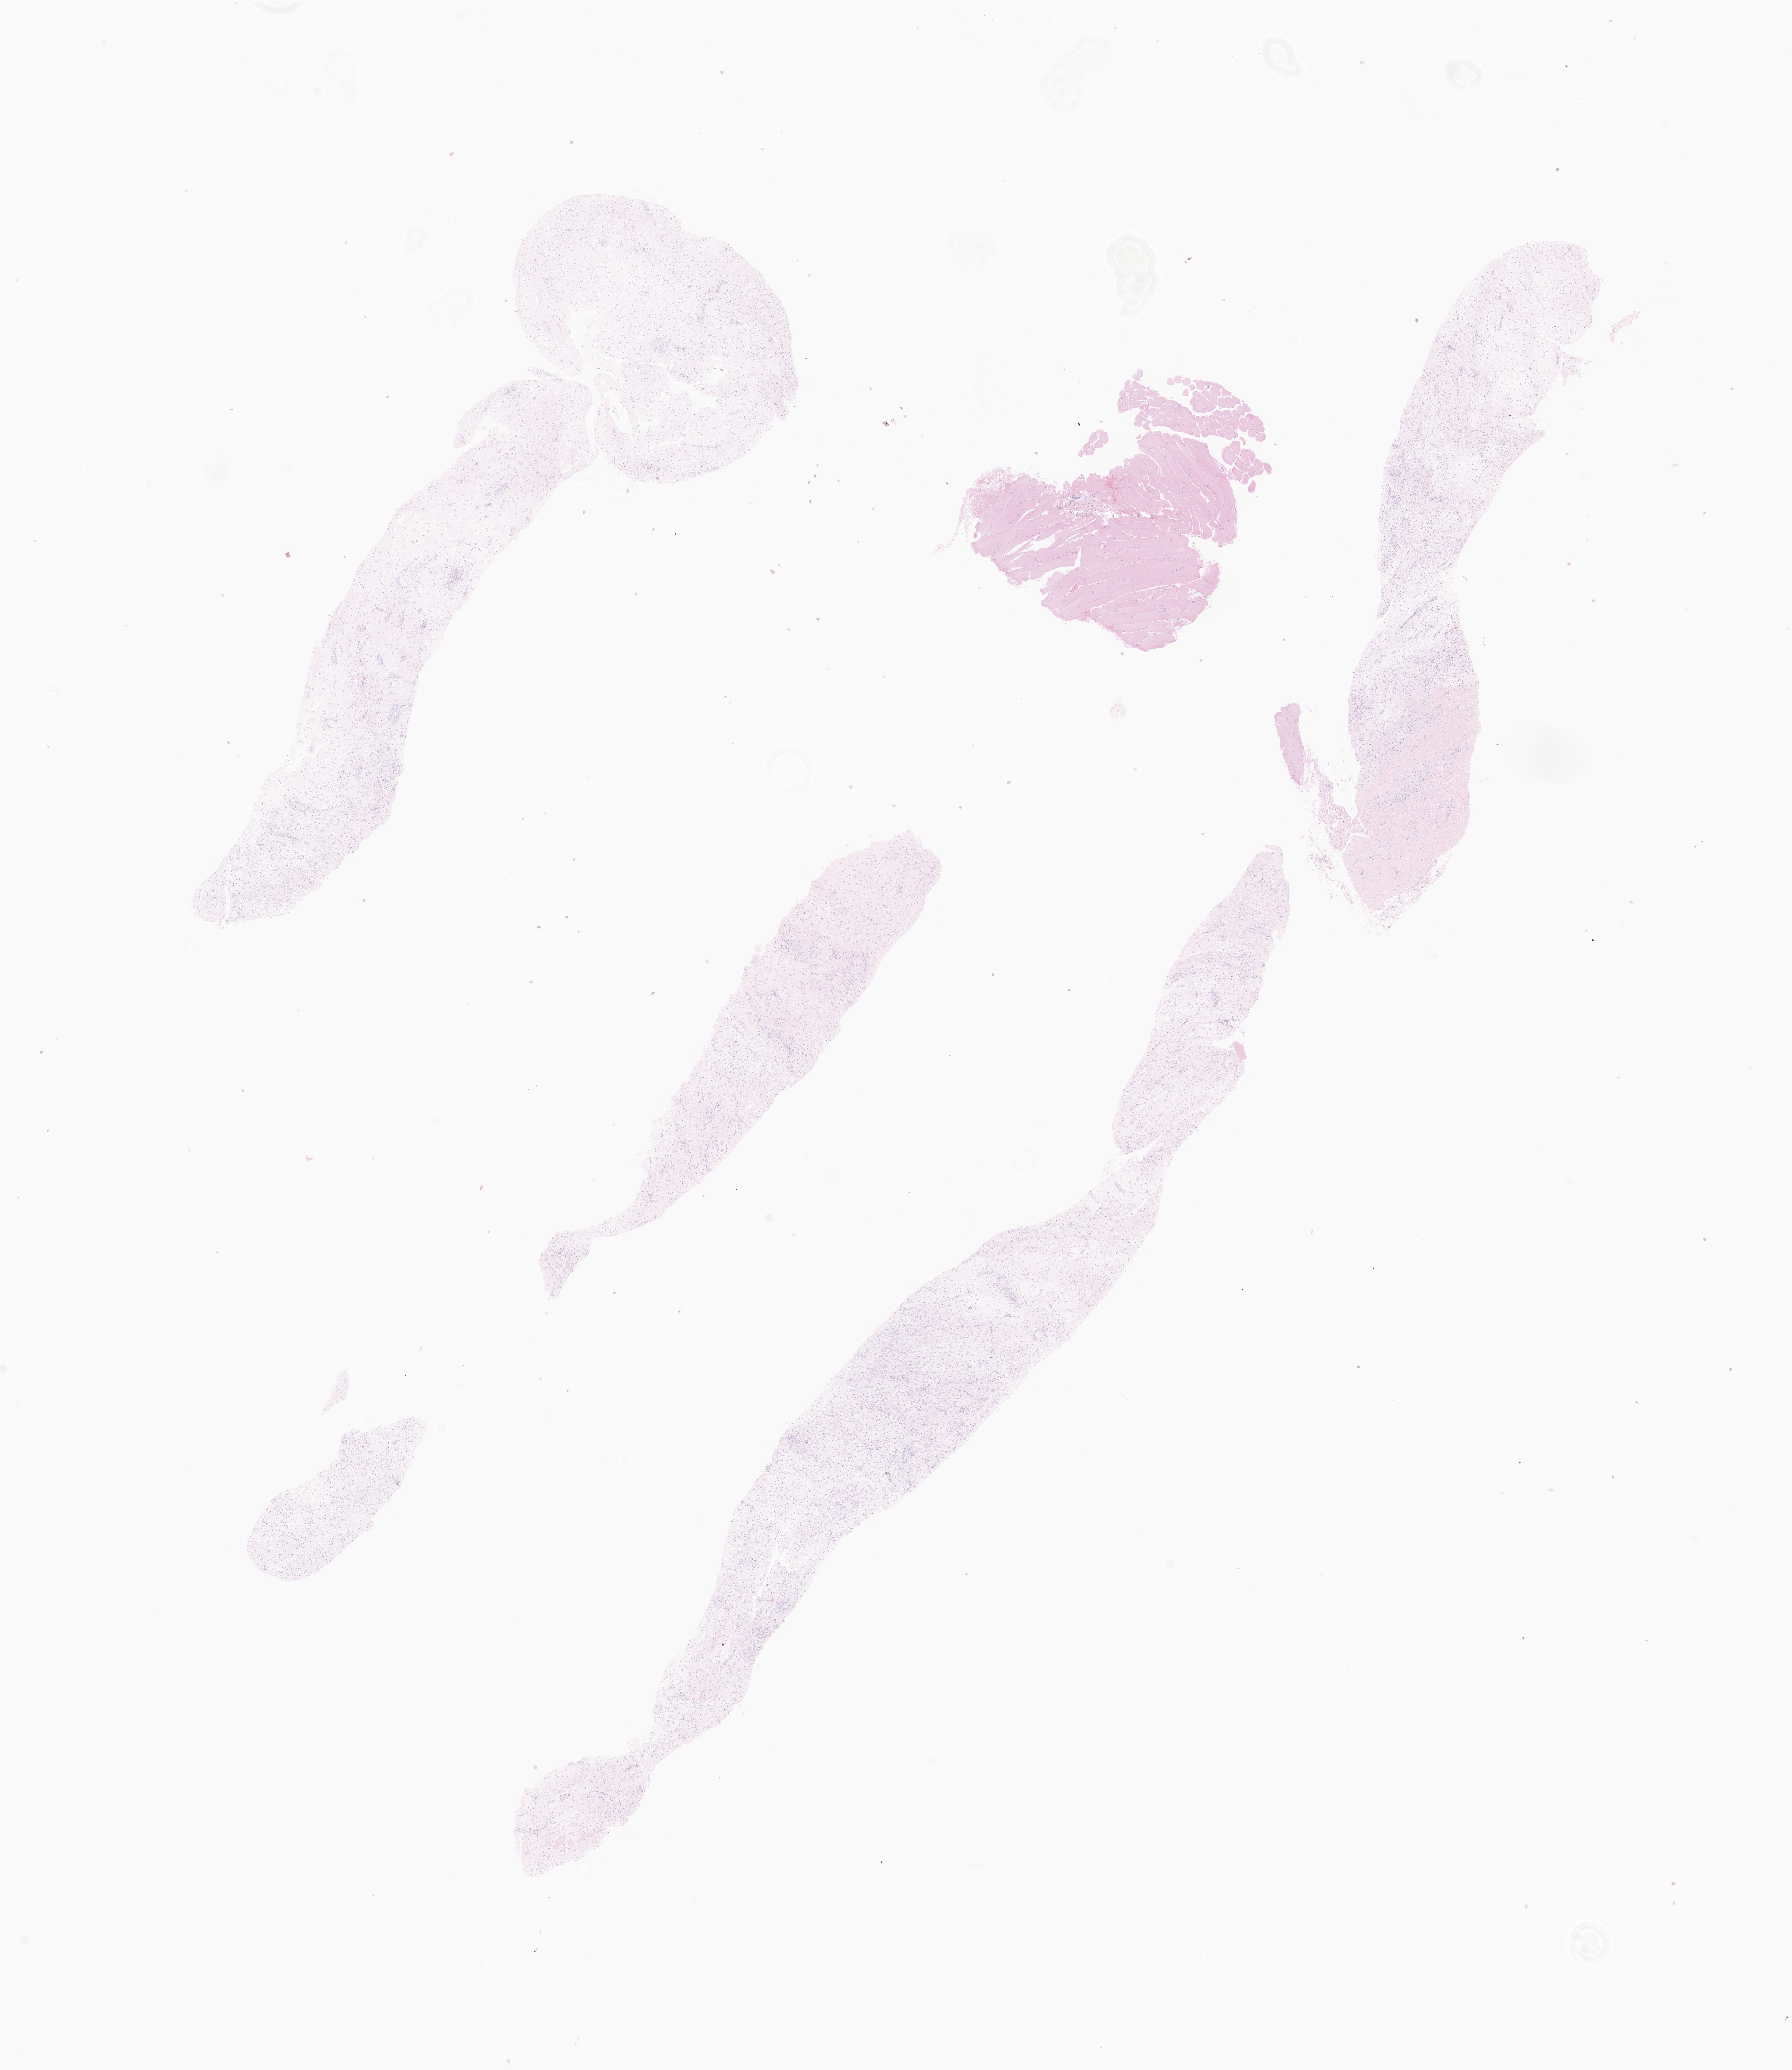
Whole-slide image, hematoxylin and eosin (H&E) stain of tumor tissue from the long bone of lower limb, whole scanned area (about 17.1 x 19.8 mm) shown as a low-resolution overview, formalin-fixed, paraffin-embedded (FFPE) tissue. Patient female; age 203 months (16 years 11 months).
* diagnosis (ICD-O-3 morphology term): Neoplasm, malignant